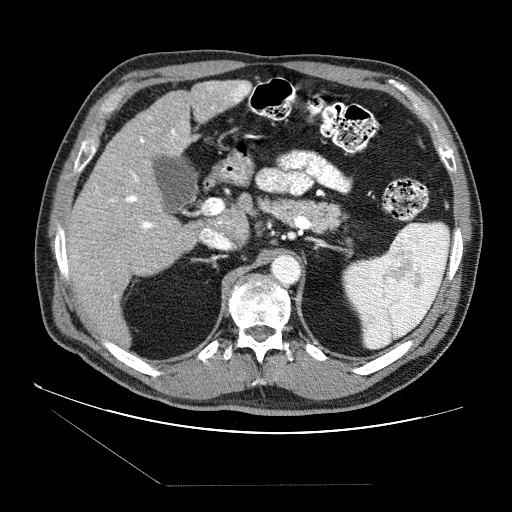
Contrast-enhanced abdominal CT (liver protocol), one axial slice; position 44 of 87 along the scan axis; reconstruction kernel STANDARD; 120 kVp; soft-tissue window (W 400 / L 40 HU); 2.5 mm slice thickness; 512 × 512 image matrix, field of view 400 × 400 mm. Case-level facts recorded for this patient, not image findings: diagnosis: hepatocellular carcinoma (patient treated with transarterial chemoembolisation; whether this scan precedes or follows treatment is not stated here); TNM stage (as recorded): Stage-II; Child-Pugh class: B; tumour nodularity: multinodular; tumour size: 2.6 cm.
Outlined on this slice (semi-automatically segmented with operator editing):
- liver parenchyma outside the tumour (the mass and vessels are separate outlines, so this box may not span the whole liver): bounding box [x1, y1, x2, y2] px = [64, 80, 250, 340]
- liver vessels: [64, 81, 250, 297]